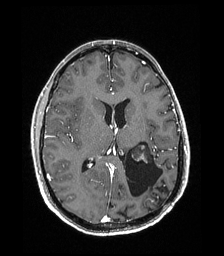
Brain MRI from a brain-tumour surgery series, one axial slice. Position 90 of 192 along the scan axis. T1-weighted post-contrast. 1 mm slice thickness. 224 × 256 image matrix, field of view 224 × 256 mm. Case-level facts recorded for this patient, not image findings: histopathology: Low grade glioma; IDH mutation: no; tumour location: Left Parieto-Occipital Intraventricular.
Annotated regions visible in this slice (expert manual segmentation):
- previous resection cavity: bounding box [x1, y1, x2, y2] px = [125, 141, 163, 203]
- tumour: [131, 144, 149, 170]